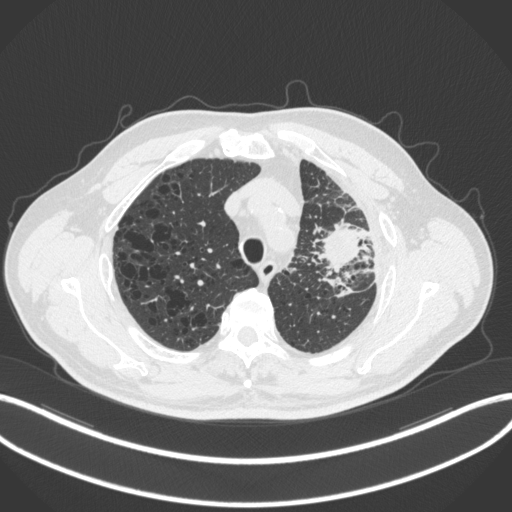
Chest CT, one axial slice; slice 241 of 286 in the series (ordered by position); reconstruction kernel B31f; lung window (W 1500 / L -600 HU); 512 × 512 image matrix. Male patient, age 68 years. Case-level facts recorded for this patient, not image findings: clinical TNM (as recorded): T3 N3 M1.
Outlined on this slice (bounding box drawn by a radiologist):
- lung tumour (recorded histology: adenocarcinoma): bounding box (x1, y1, x2, y2) in pixels: (318, 221, 361, 275)